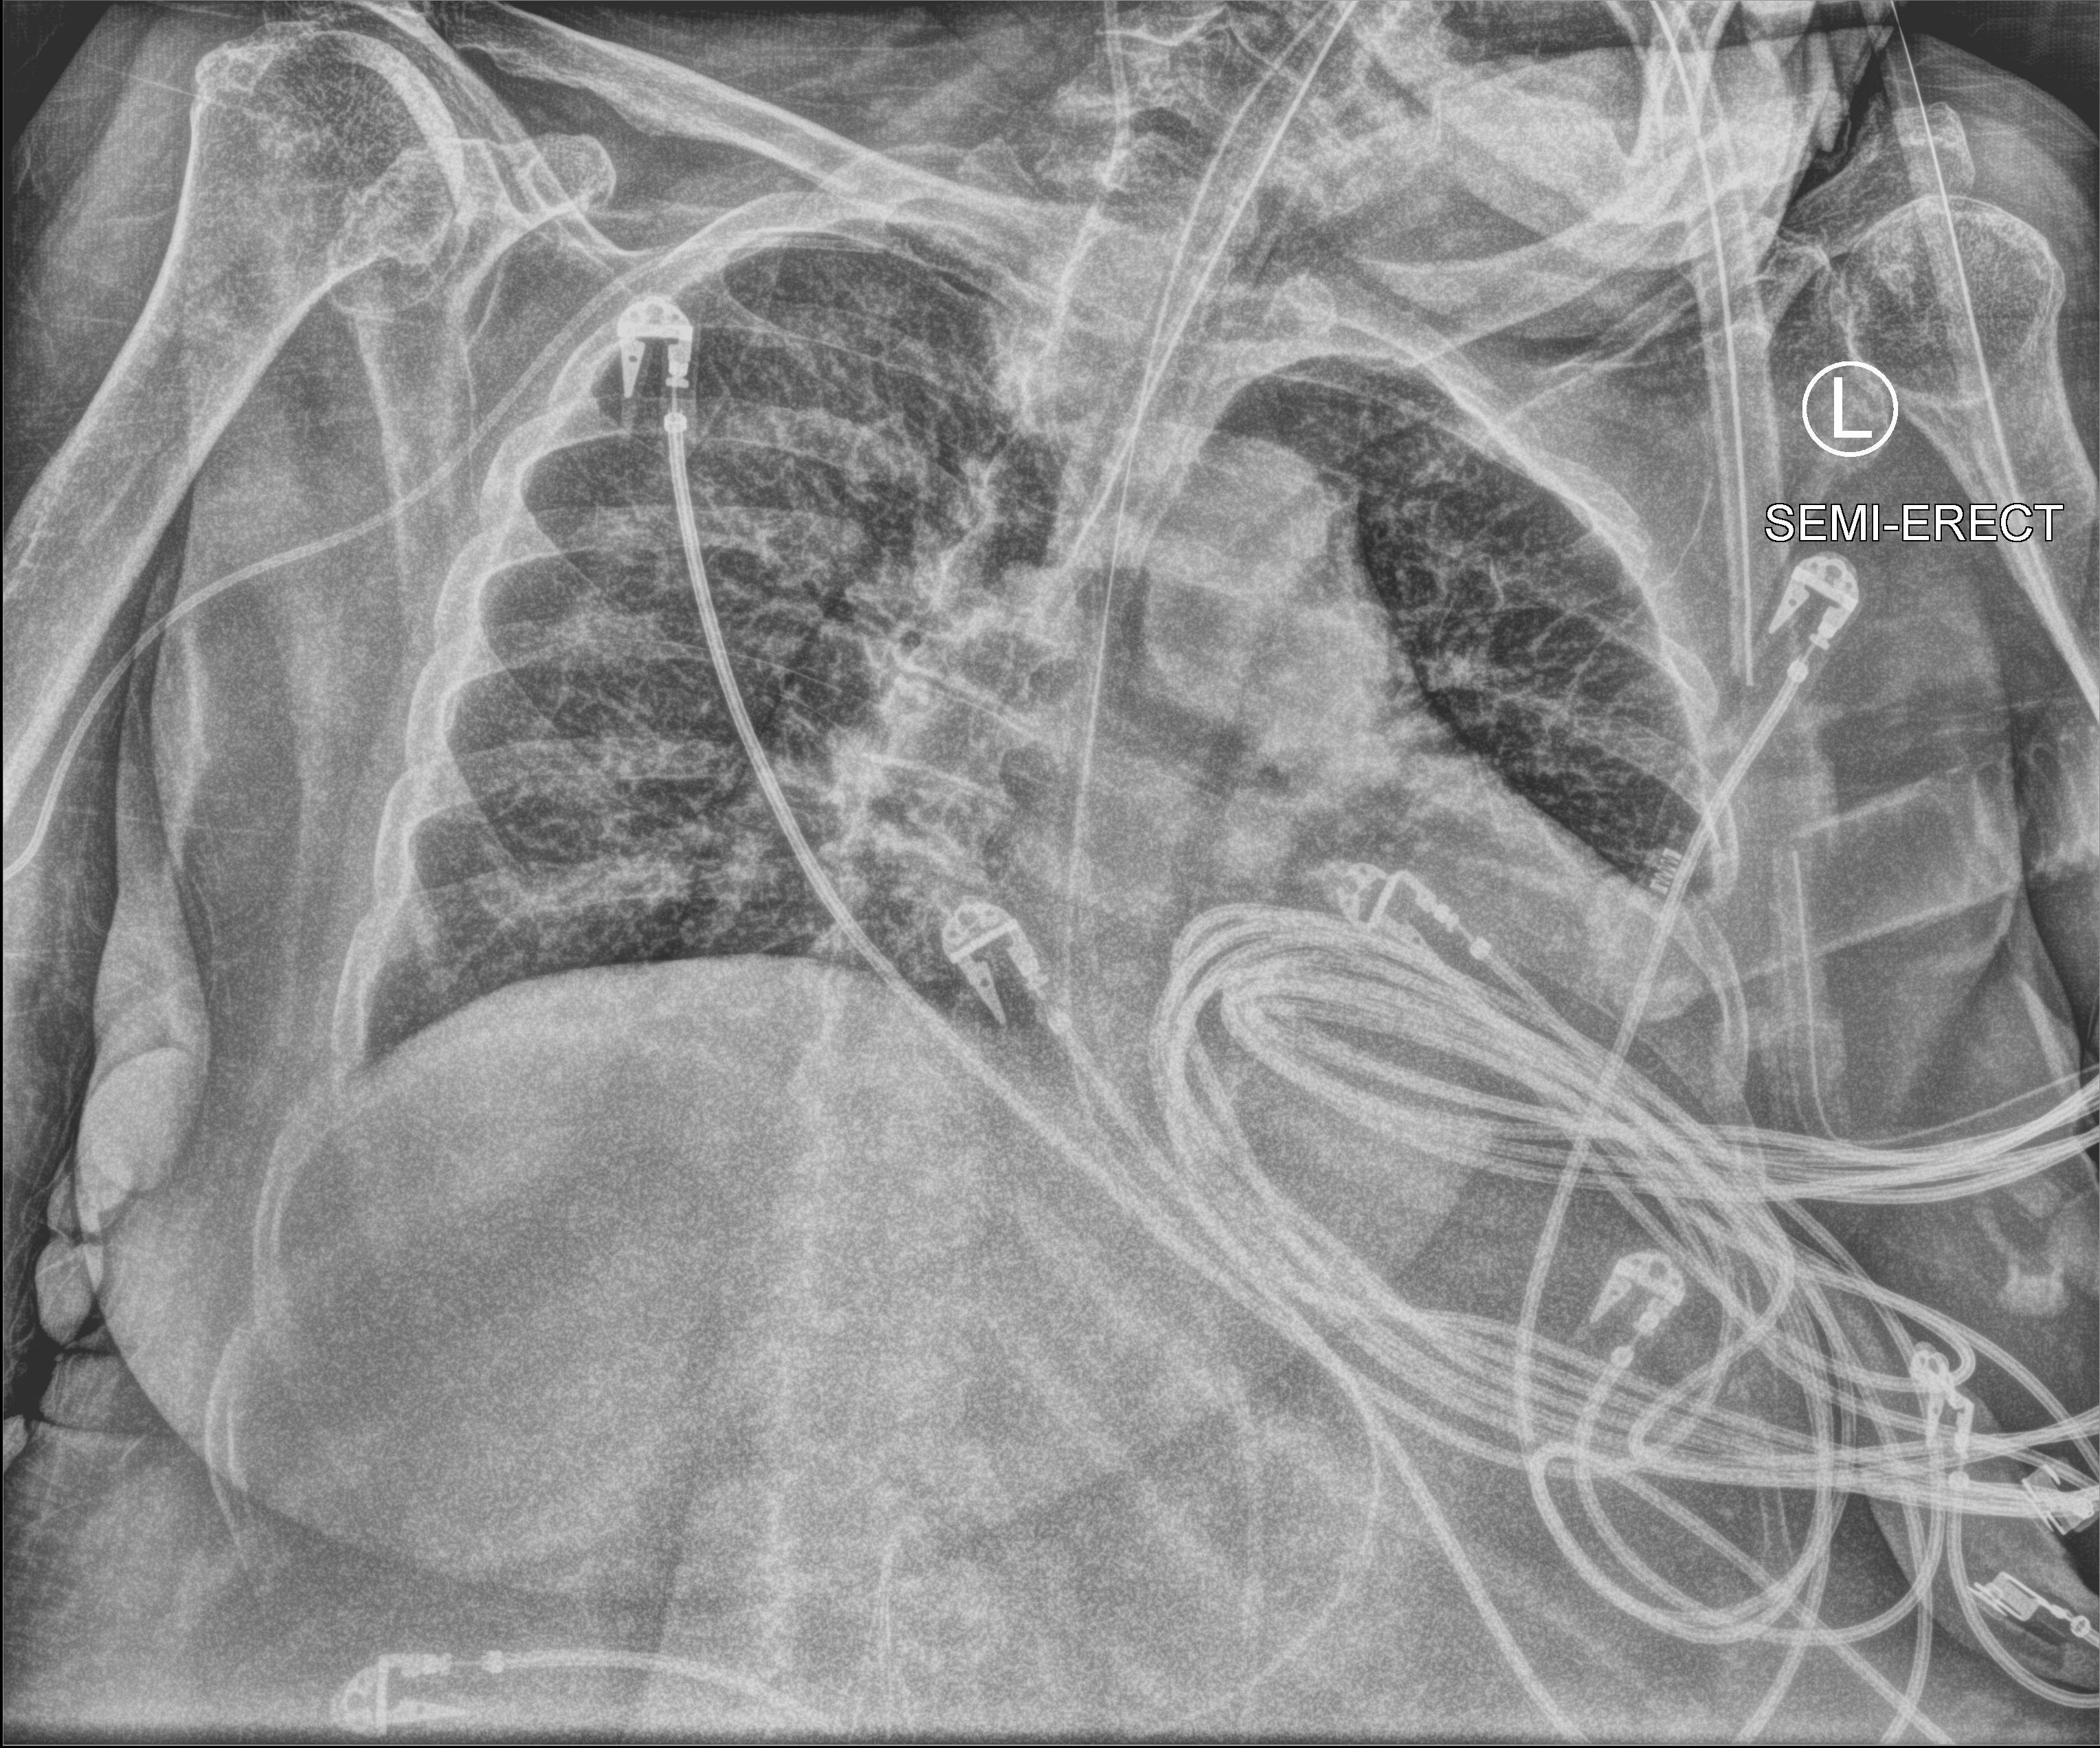
Portable chest radiograph; anteroposterior (AP) projection. Patient hospitalised with COVID-19; female, aged 75–90 years.
Admission-level facts for this patient (not findings on this image; timing relative to this image not recorded): diabetes (admission record): yes.